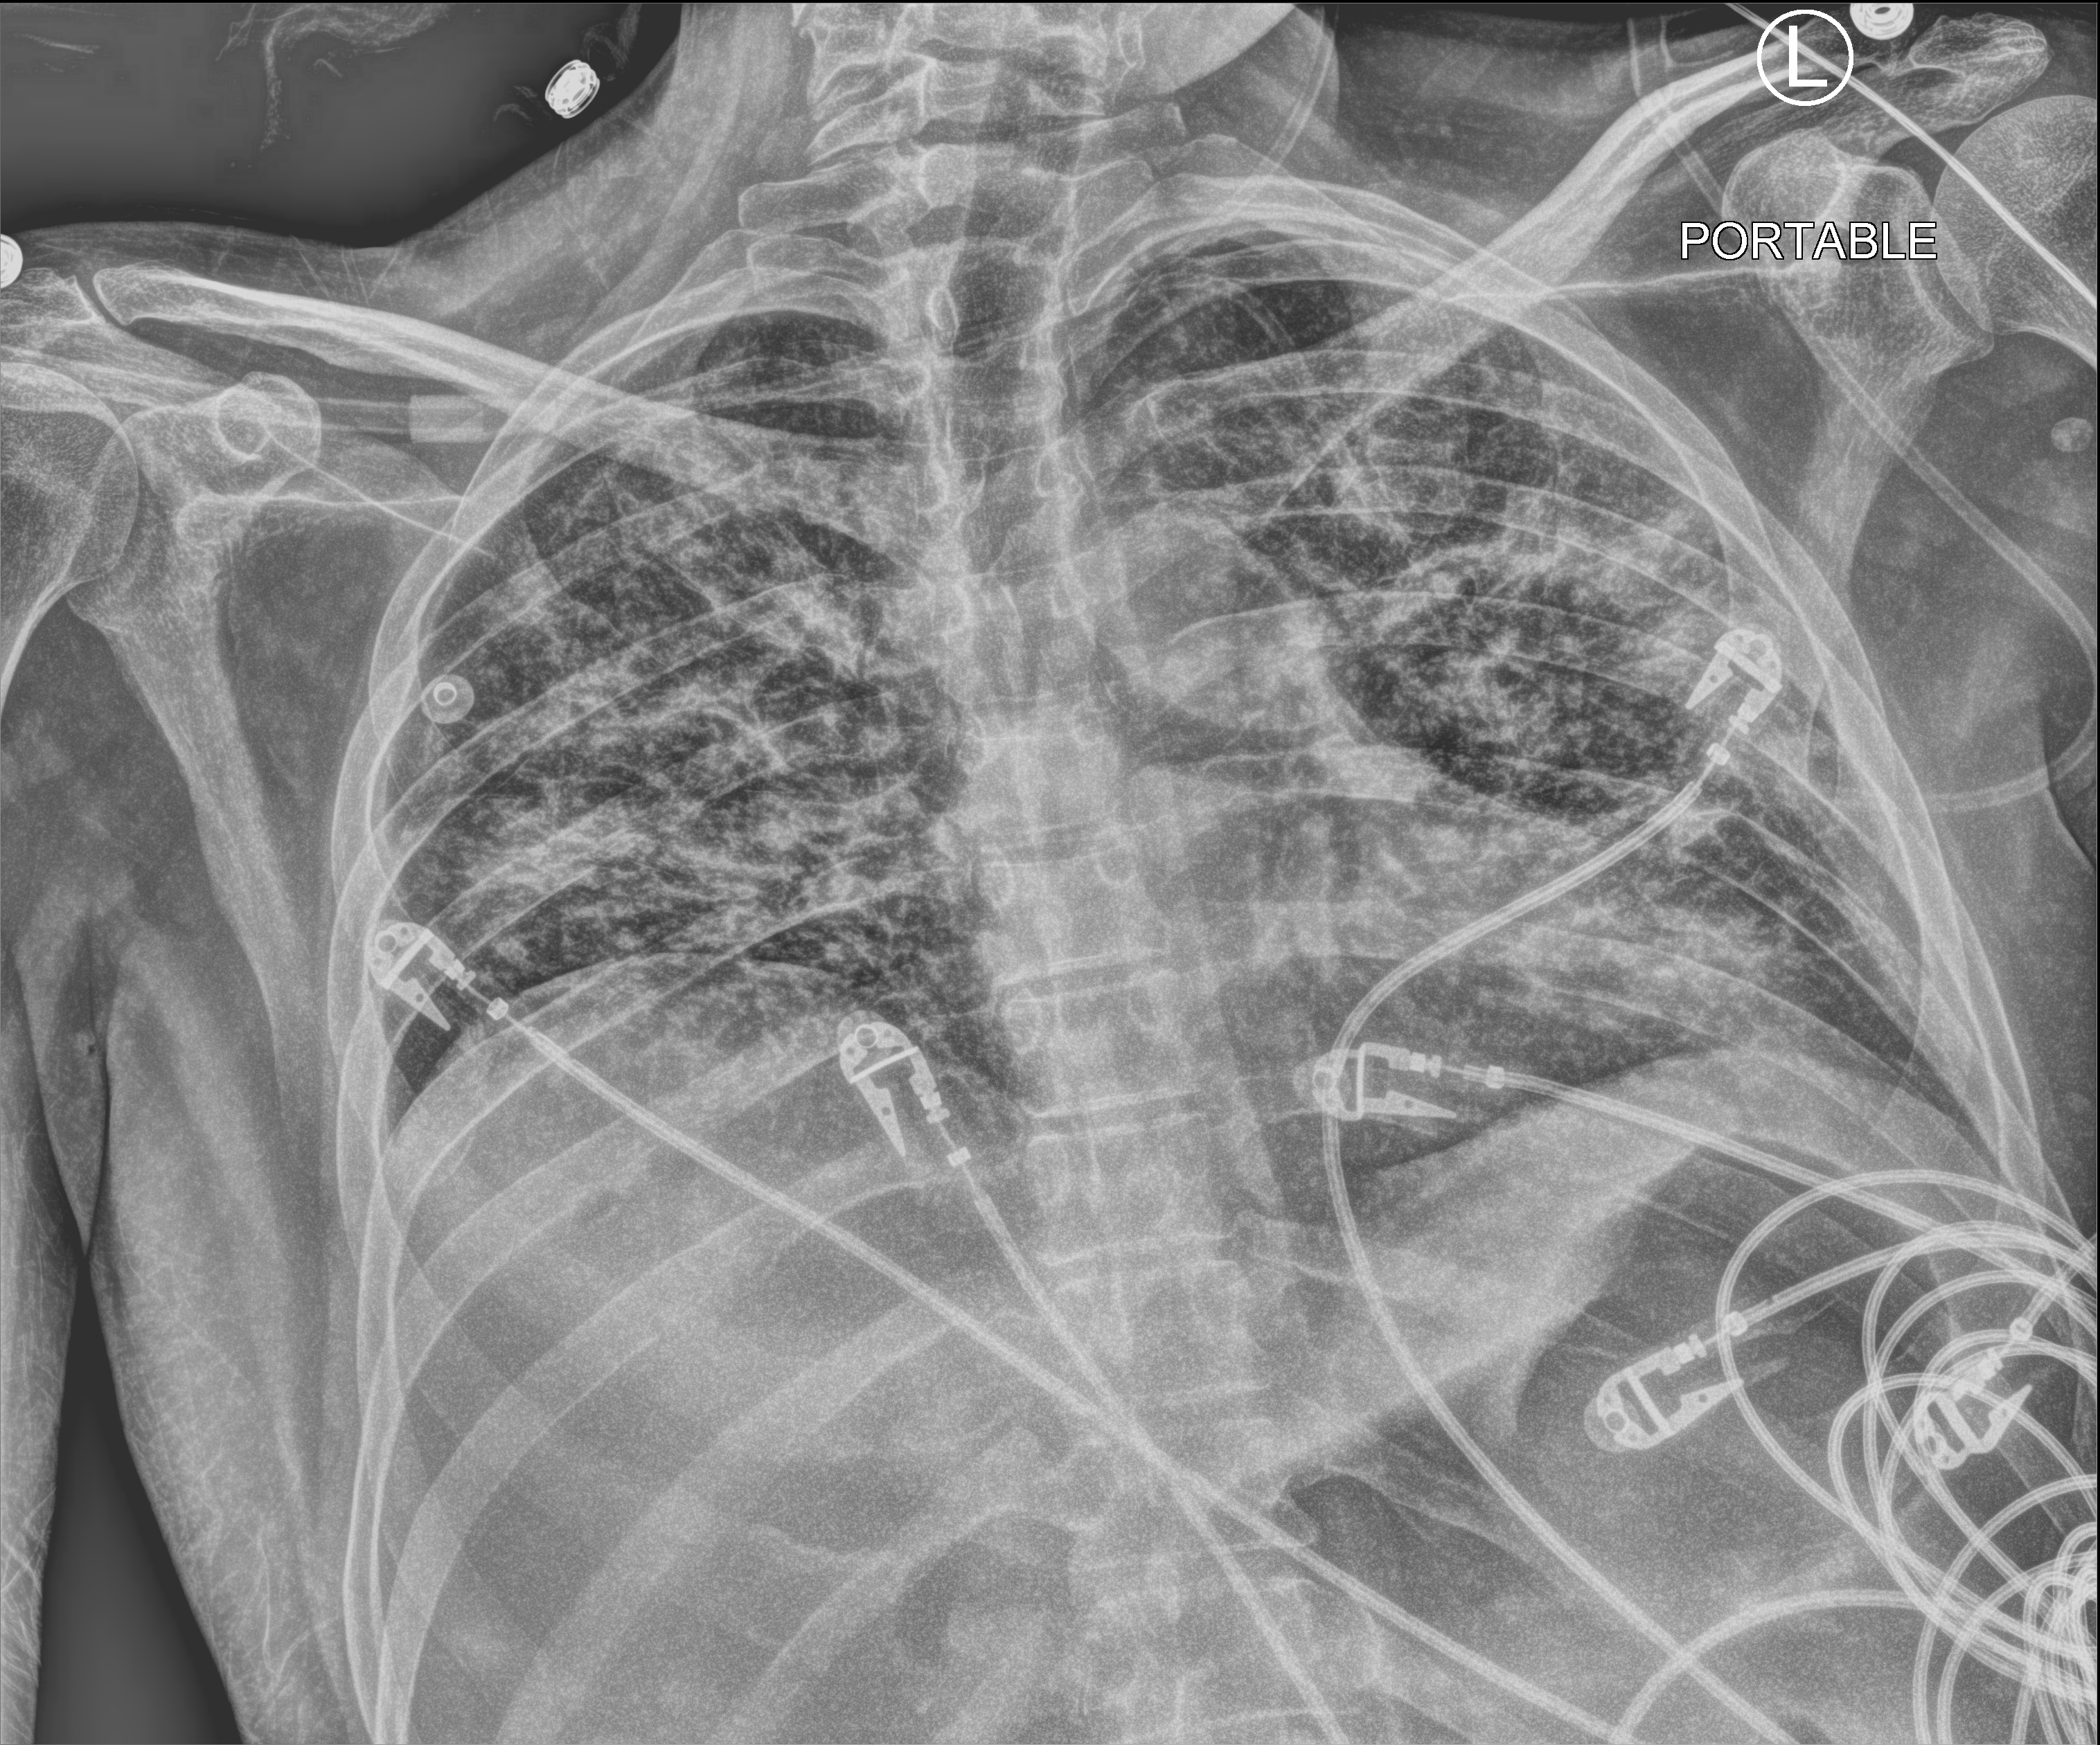
Chest X-ray (portable); anteroposterior (AP) projection. Male patient hospitalised with COVID-19, age 18–59 years.
From the hospital-stay record, not from the radiograph (when in the stay this image was taken is not recorded): mechanically ventilated during this hospital stay: yes; admitted to intensive care during this hospital stay: yes; length of hospital stay: 48 days.